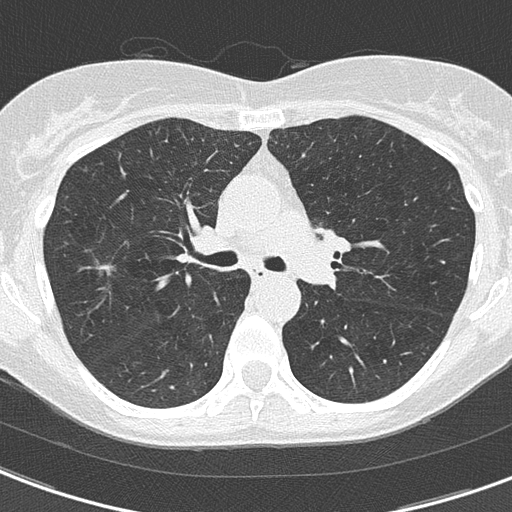
Low-dose screening chest CT, axial slice; second annual screen; lung window (W 1500 / L -600 HU); 2 mm slice thickness; 120 kVp; slice 58 of 156 in the series; 512 × 512 image matrix, field of view 280 × 280 mm. Female participant, aged 59 years at enrolment. Current smoker at enrolment.
- Lesion marked by an expert reader, bounding box [x1, y1, x2, y2] px = [77, 249, 139, 296].
- The exam's reader record, not a measurement of the box and not confirmed to be the same lesion: non-calcified nodule or mass ≥4 mm, right upper lobe, 7 × 6 mm, poorly defined margins, ground glass attenuation, pre-existing on the prior screen: yes; interval growth: no.
- Participant outcome: lung cancer diagnosed 454 days after this screen — bronchiolo-alveolar adenocarcinoma, NOS, right upper lobe, well differentiated (G1), stage IA (AJCC 6th edition), 4 mm at pathology.